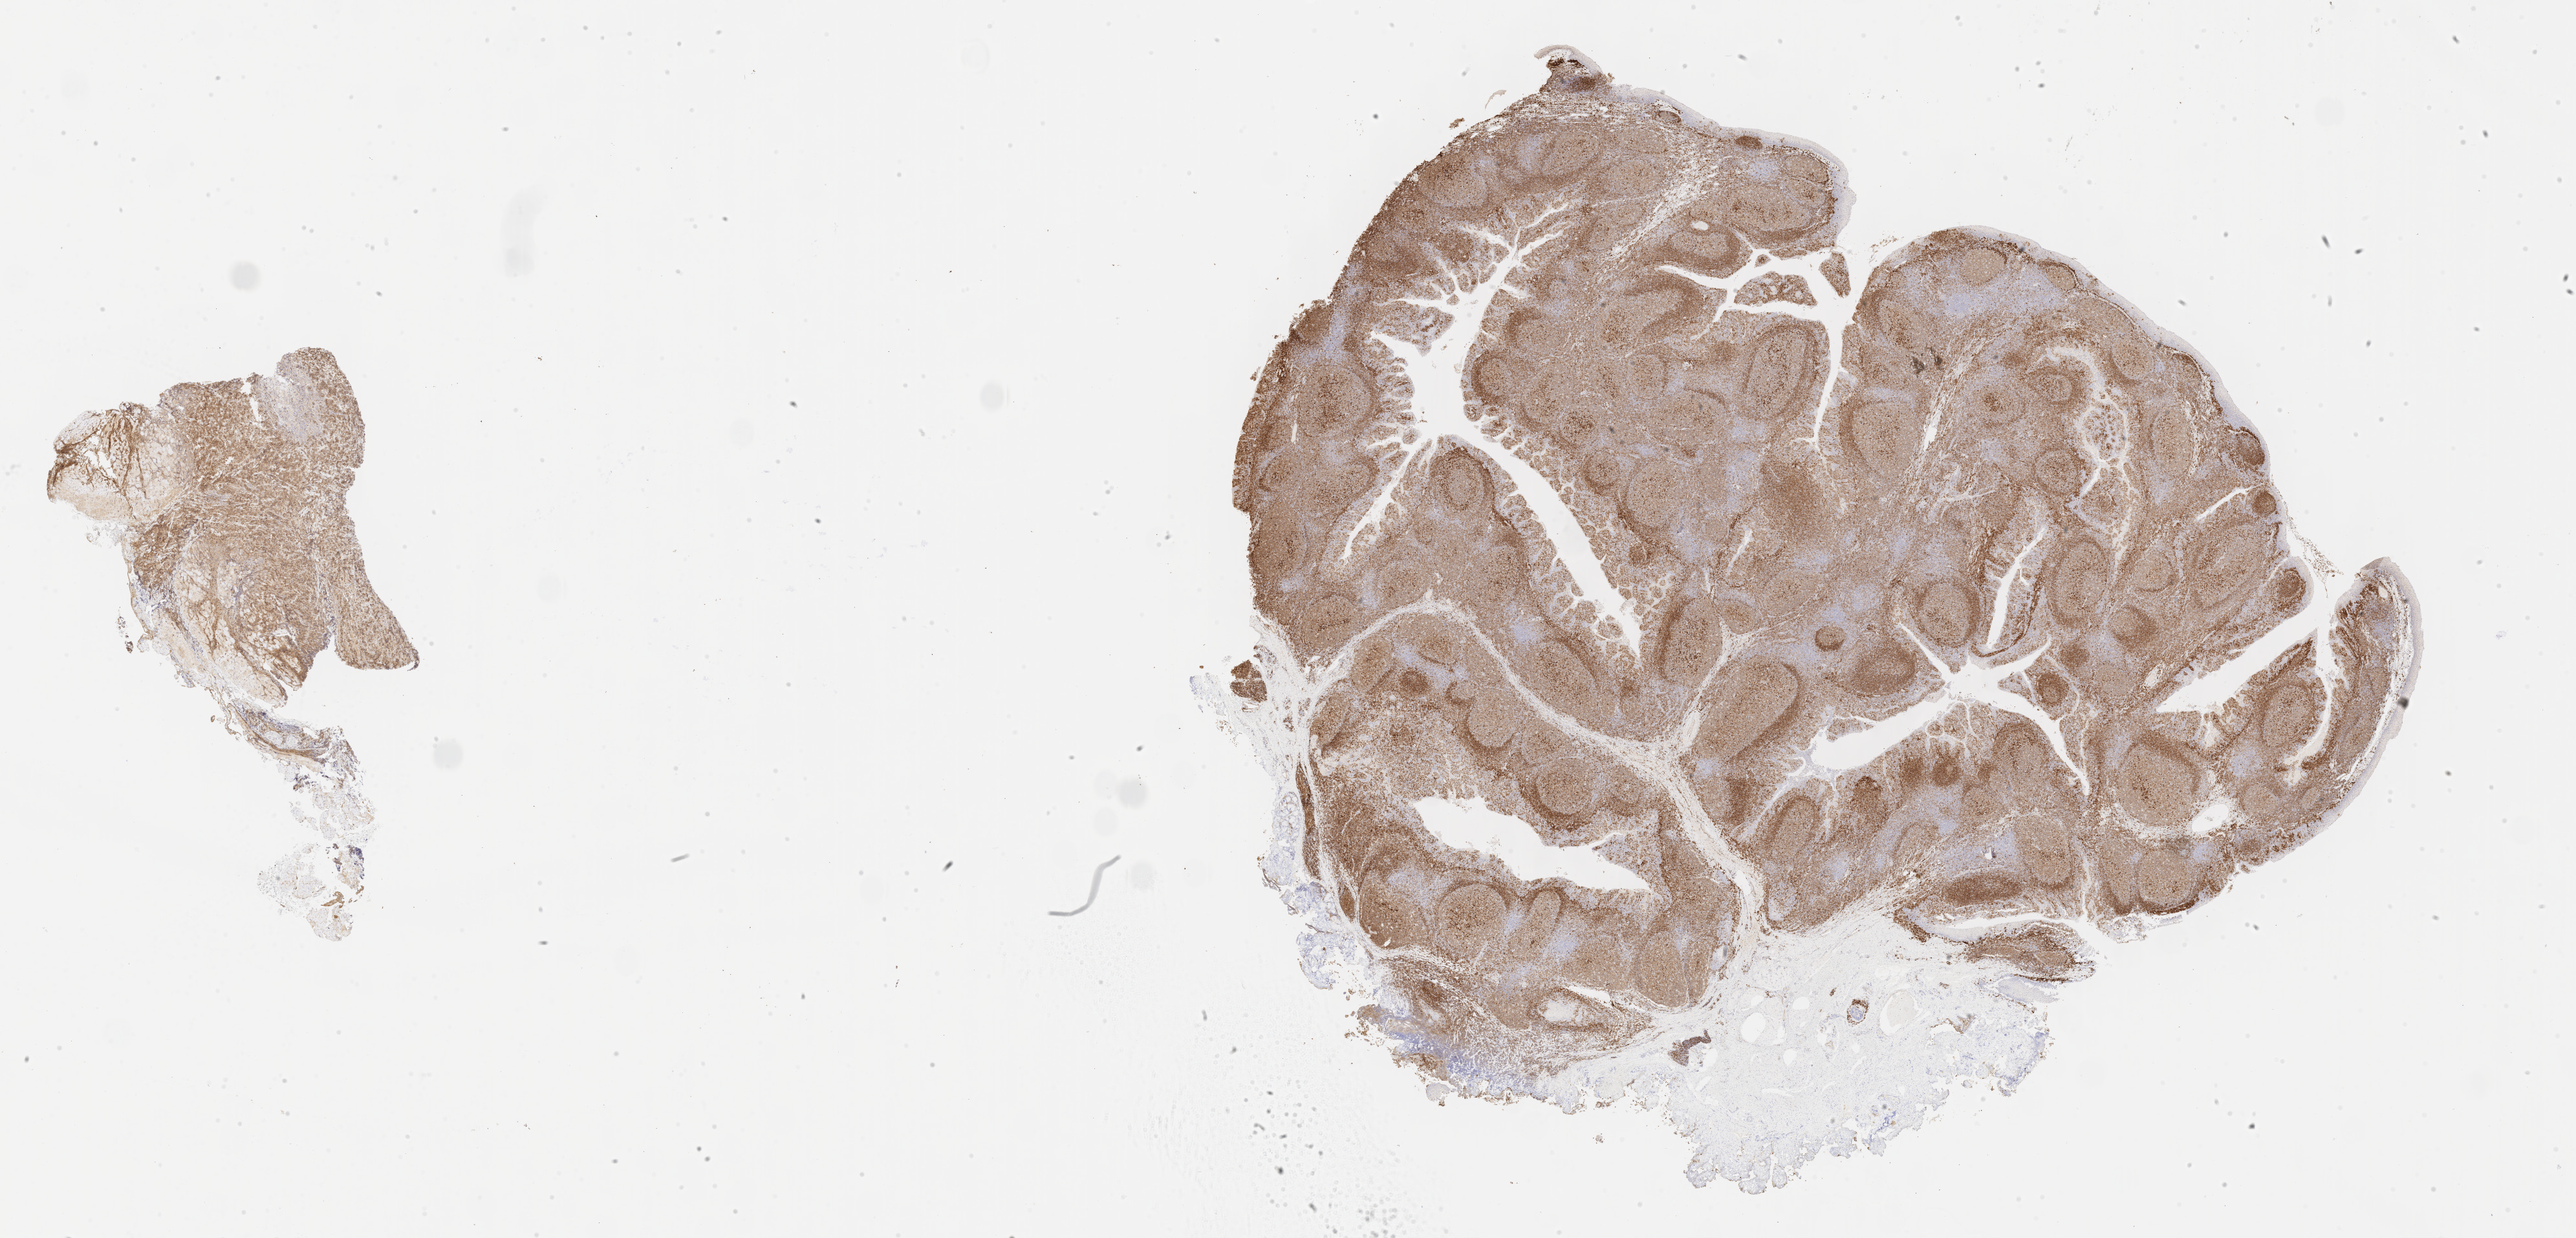
Whole-slide image, immunohistochemical stain for CD79a — shown as a low-resolution overview of the whole scanned area (about 32.2 x 15.5 mm). Tumor tissue. Site: kidney. Patient: male, aged 12.
* histologic diagnosis: Diffuse large B-cell lymphoma, NOS